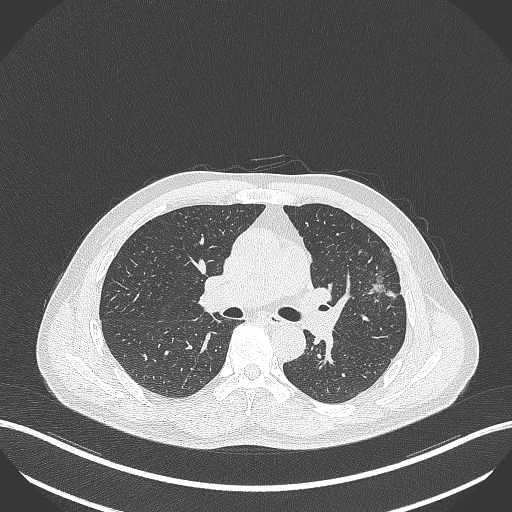
Chest CT, one axial slice; position 234 of 418 along the scan axis; reconstruction kernel B70f; lung window (W 1500 / L -600 HU); 1 mm slice thickness; 512 × 512 image matrix, field of view 400 × 400 mm. Patient: male, 55 years. Case-level facts recorded for this patient, not image findings: clinical TNM (as recorded): T1c N0 M0.
Structures marked on this image (rectangle marked by the reading radiologist):
- lung tumour (recorded histology: adenocarcinoma): bounding box (x1, y1, x2, y2) in pixels: (367, 269, 399, 303)